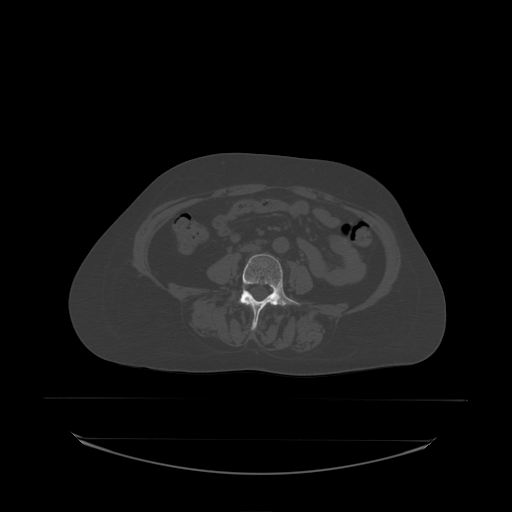
CT including the spine, one axial slice. Position 50 of 242 along the scan axis. Bone window (W 1800 / L 400 HU). 2.5 mm slice thickness. 512 × 512 image matrix. Patient: female, 53 years. Case-level facts recorded for this patient, not image findings: primary cancer: lung.
Annotated regions visible in this slice (semi-automatically segmented with operator editing):
- L4 vertebra: box from (x=240, y=254) to (x=301, y=331) px